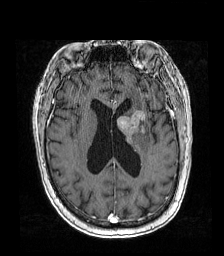
Brain MRI from a brain-tumour surgery series, one axial slice. Position 72 of 192 along the scan axis. T1-weighted post-contrast. 1 mm slice thickness. 224 × 256 image matrix, field of view 219 × 250 mm. Case-level facts recorded for this patient, not image findings: histopathology: Metastatic carcinoma from lung primary.
Outlined on this slice (manually delineated by an expert):
- tumour: box from (x=117, y=110) to (x=148, y=145) px